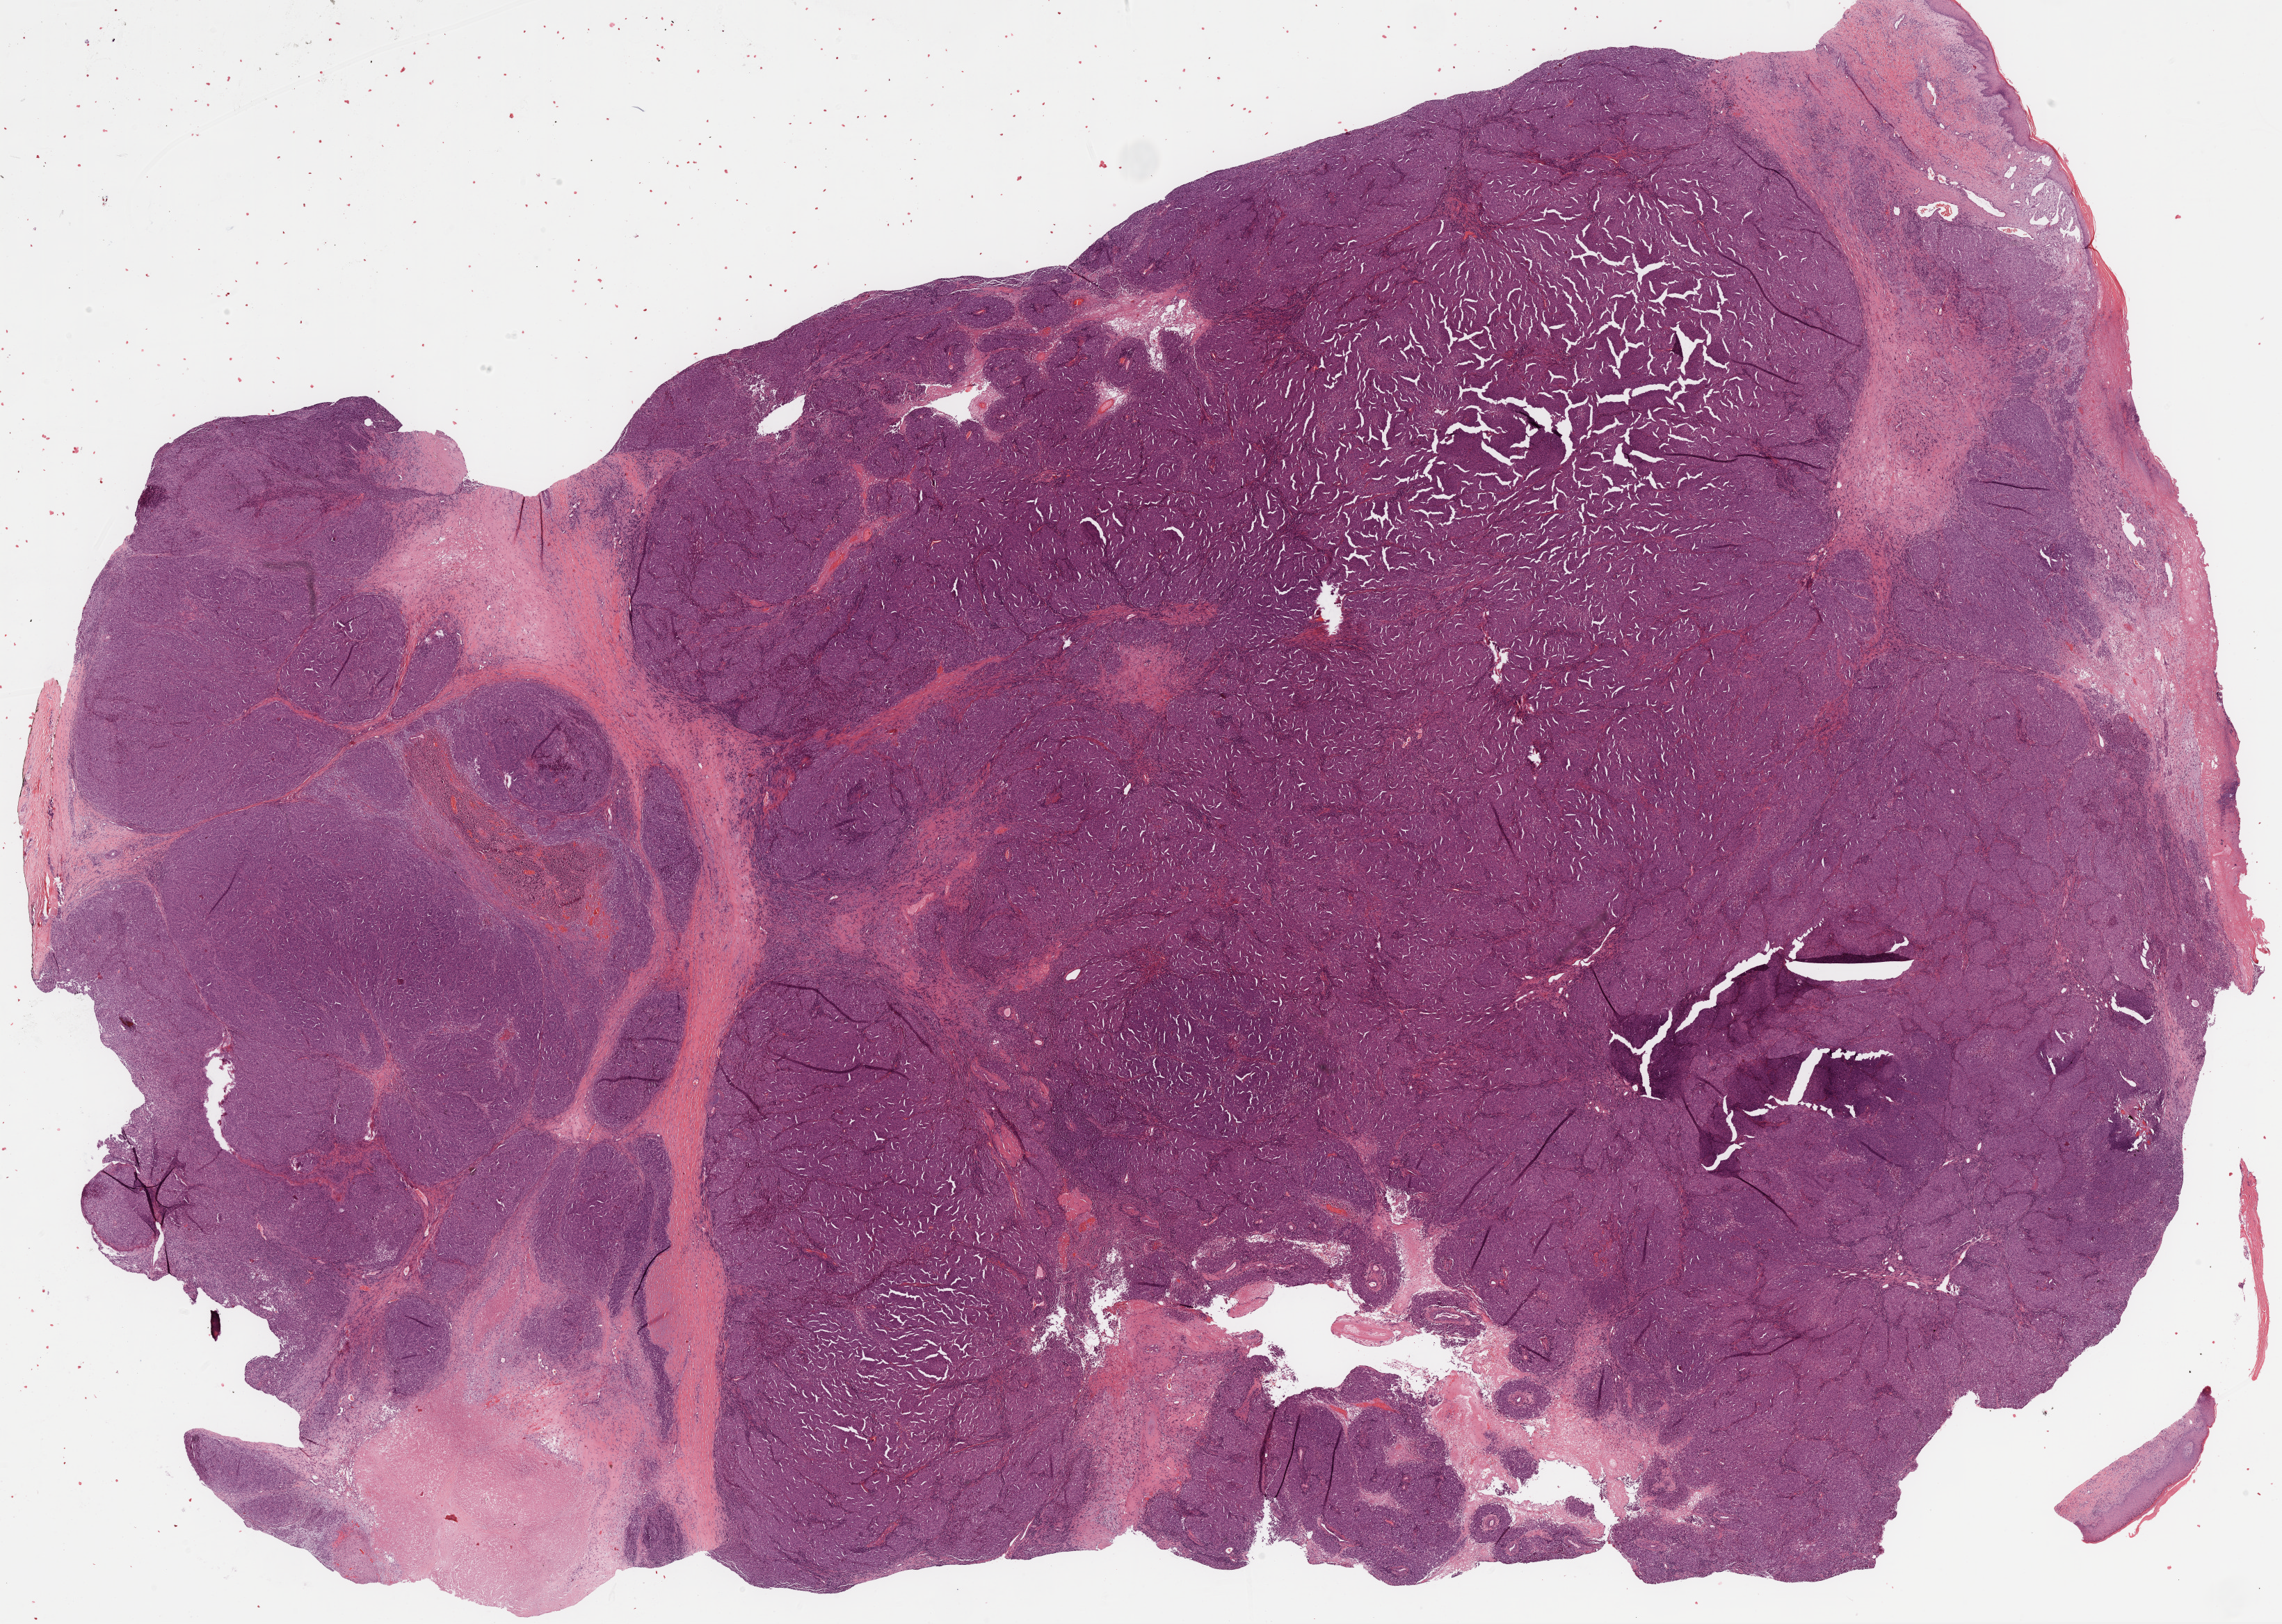
H&E whole-slide image — low-resolution overview of the scanned area, about 26.5 x 18.8 mm; formalin-fixed paraffin-embedded (FFPE) diagnostic section; metastatic tumour sample, sampled site: connective, subcutaneous and other soft tissues of lower limb and hip. Female, age 39 years at initial diagnosis.
This section: metastatic tumour tissue. Patient diagnosis: Malignant melanoma, NOS.